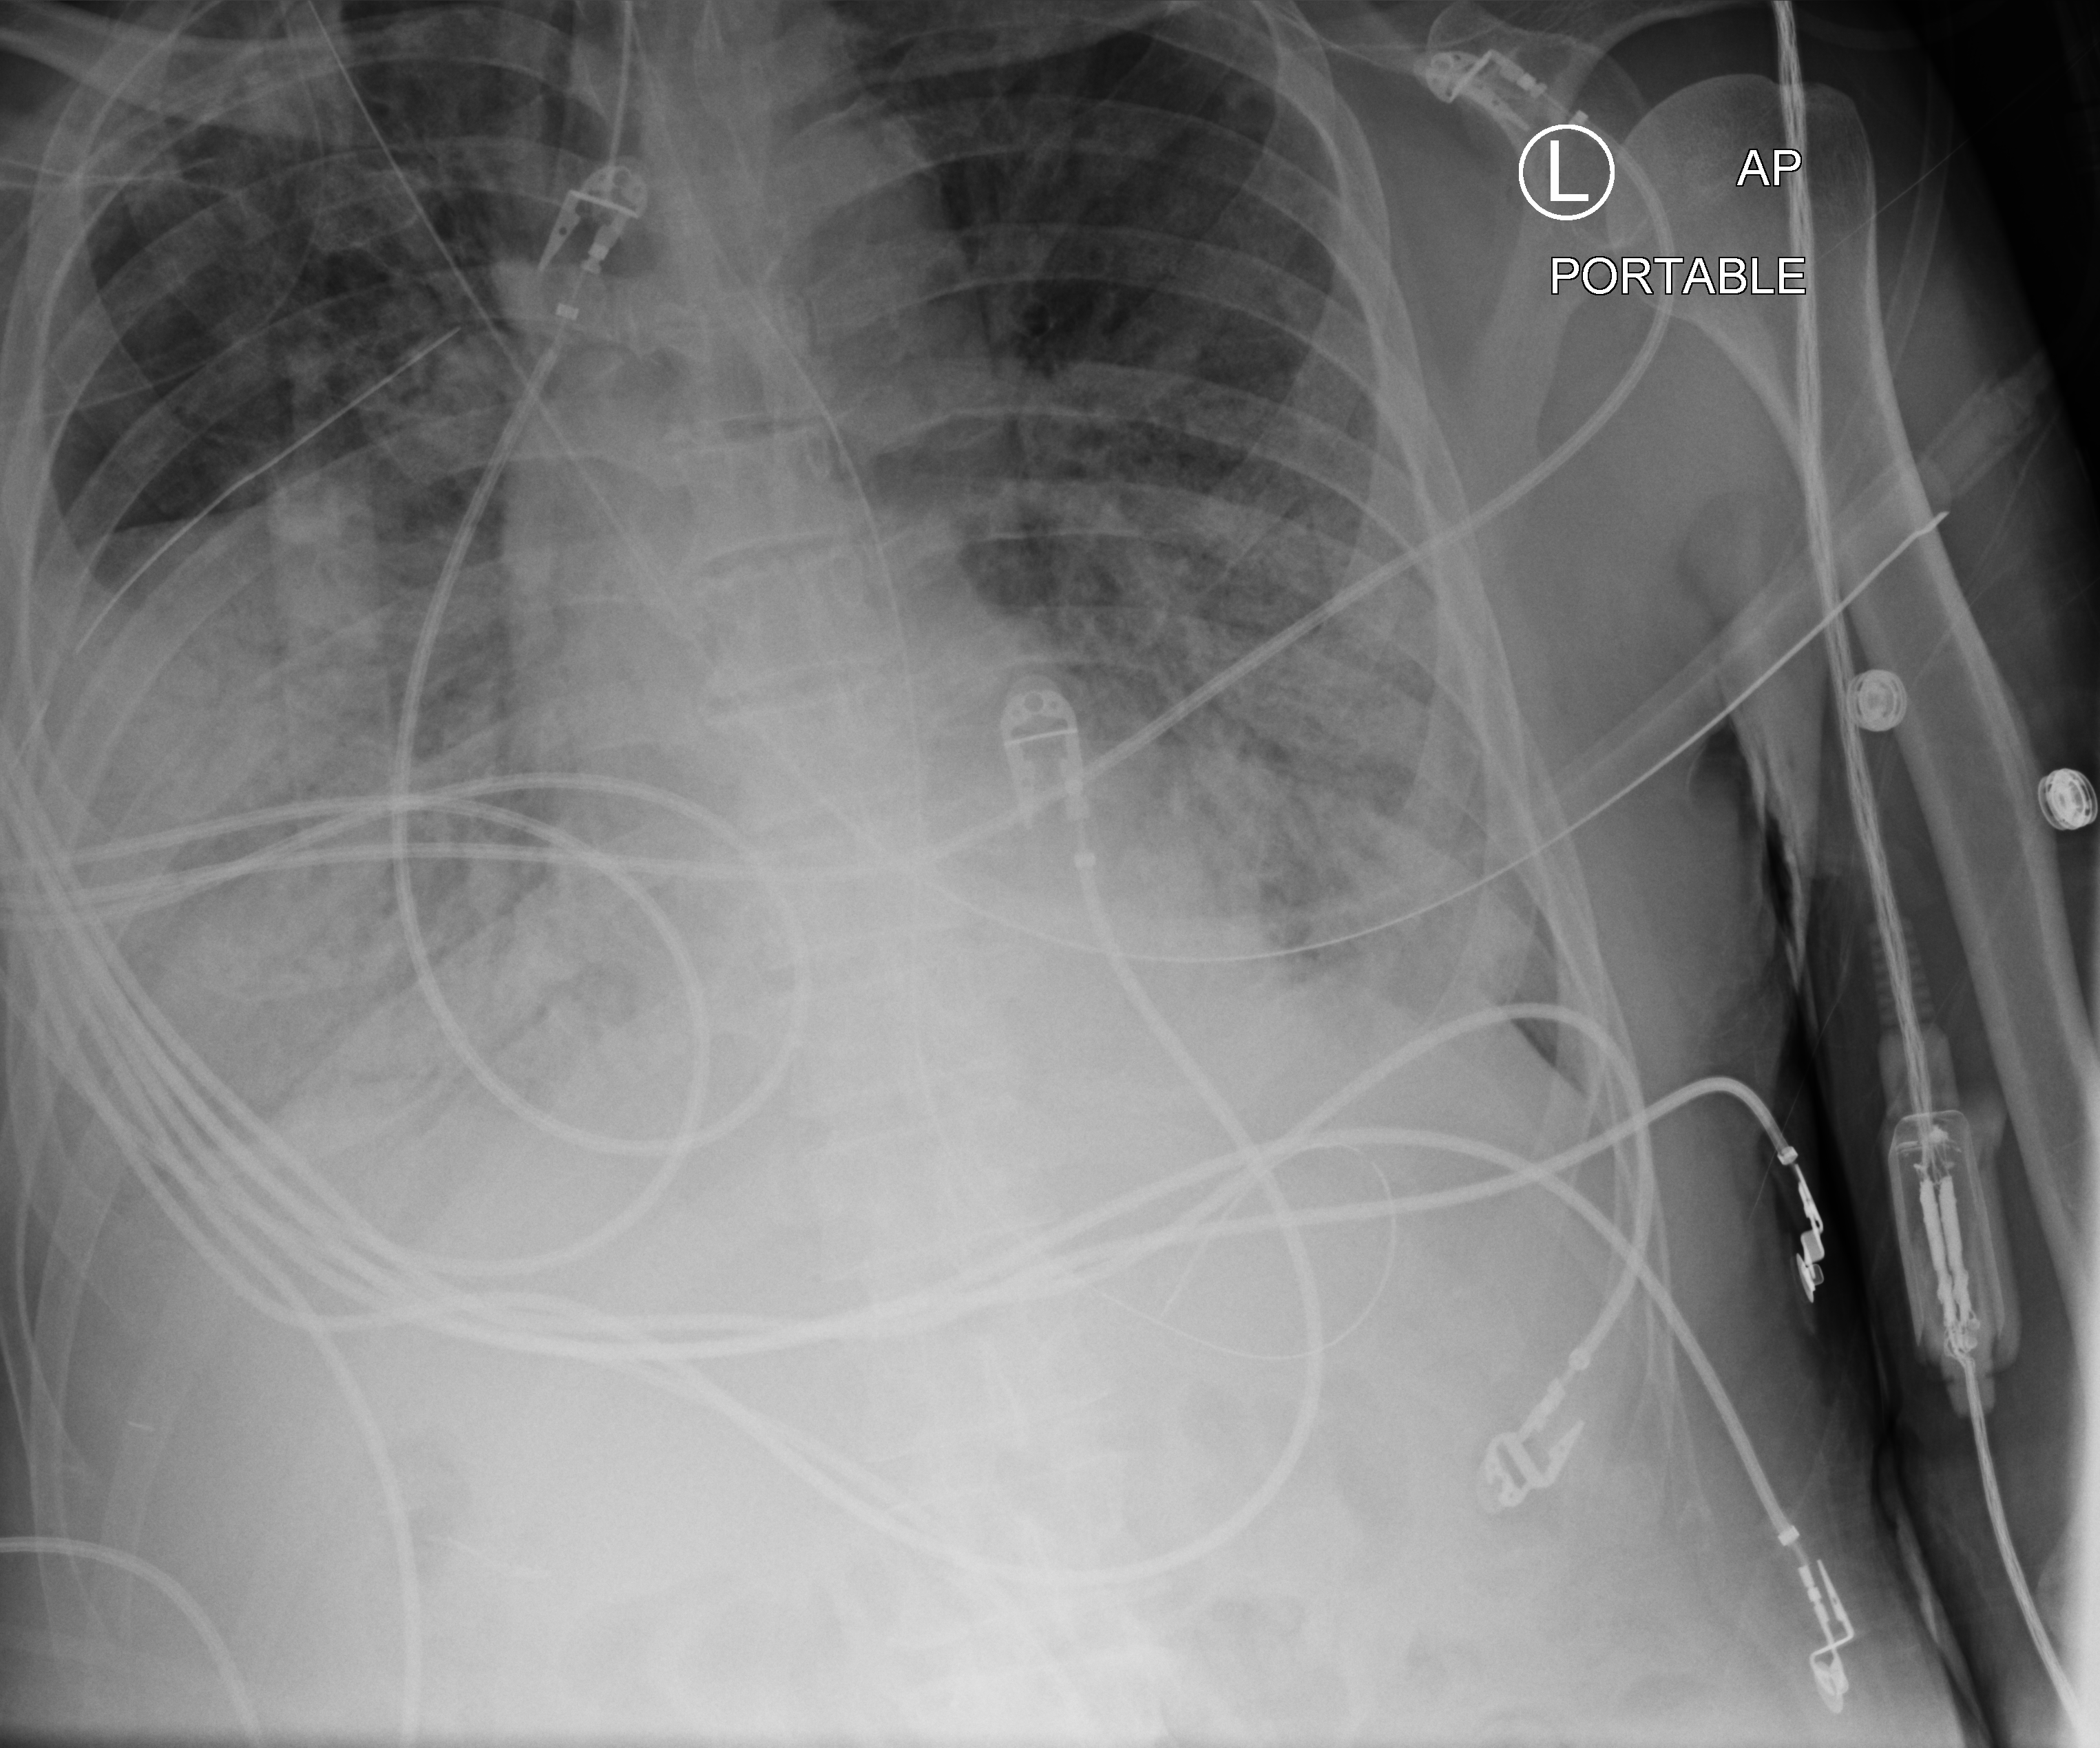
Bedside chest radiograph (computed radiography). Male patient hospitalised with COVID-19, age 60–74 years.
From the hospital-stay record, not from the radiograph (when in the stay this image was taken is not recorded):
- length of hospital stay: 31 days
- admitted to intensive care during this hospital stay: yes
- smoking status (admission record): former